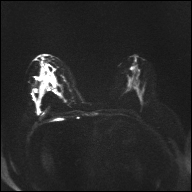
Breast MRI, one axial slice; position 17 of 32 along the scan axis; diffusion-weighted series; image 2 of 4 stored at this slice position (different b-values; order by instance number); 1.5 T; 4 mm slice thickness; 192 × 192 image matrix. Female patient.
Outlined on this slice (outlined manually by an expert reader):
- tumour on diffusion-weighted imaging: bounding box <41,71,47,76> (left, top, right, bottom; pixels)